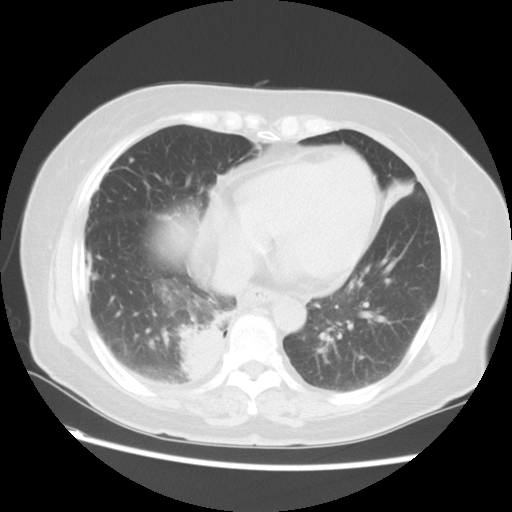
Chest CT, one axial slice. Position 23 of 57 along the scan axis. Lung window (W 1500 / L -600 HU). 5 mm slice thickness. 512 × 512 image matrix. Female patient, age 69 years. Case-level facts recorded for this patient, not image findings: clinical TNM (as recorded): T2 N1 M1a.
Structures marked on this image (rectangle marked by the reading radiologist):
- lung tumour (recorded histology: adenocarcinoma): bounding box [x1, y1, x2, y2] px = [176, 314, 230, 382]